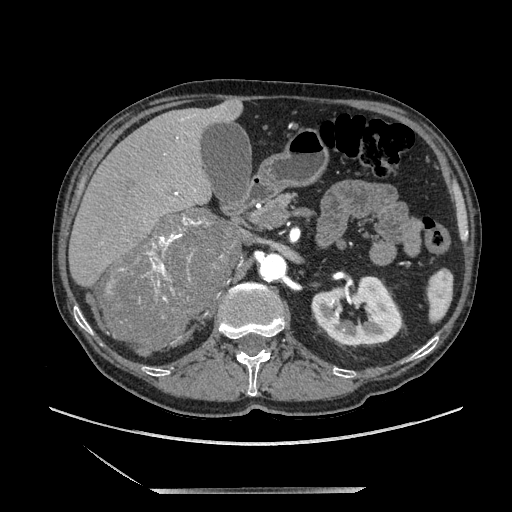
Contrast-enhanced abdominal CT, one axial slice; slice 116 of 243 in the series (ordered by position); soft-tissue window (W 400 / L 40 HU); 1.25 mm slice thickness; 512 × 512 image matrix, field of view 420 × 420 mm. Male patient. From the clinical record (not read from this slice): diagnosis: adrenocortical carcinoma; tumour side: right adrenal; tumour size at pathology: 16 cm; Ki-67 index: 17 %.
Outlined on this slice (semi-automatically segmented with operator editing):
- mass: bounding box (x1, y1, x2, y2) in pixels: (107, 208, 239, 346)